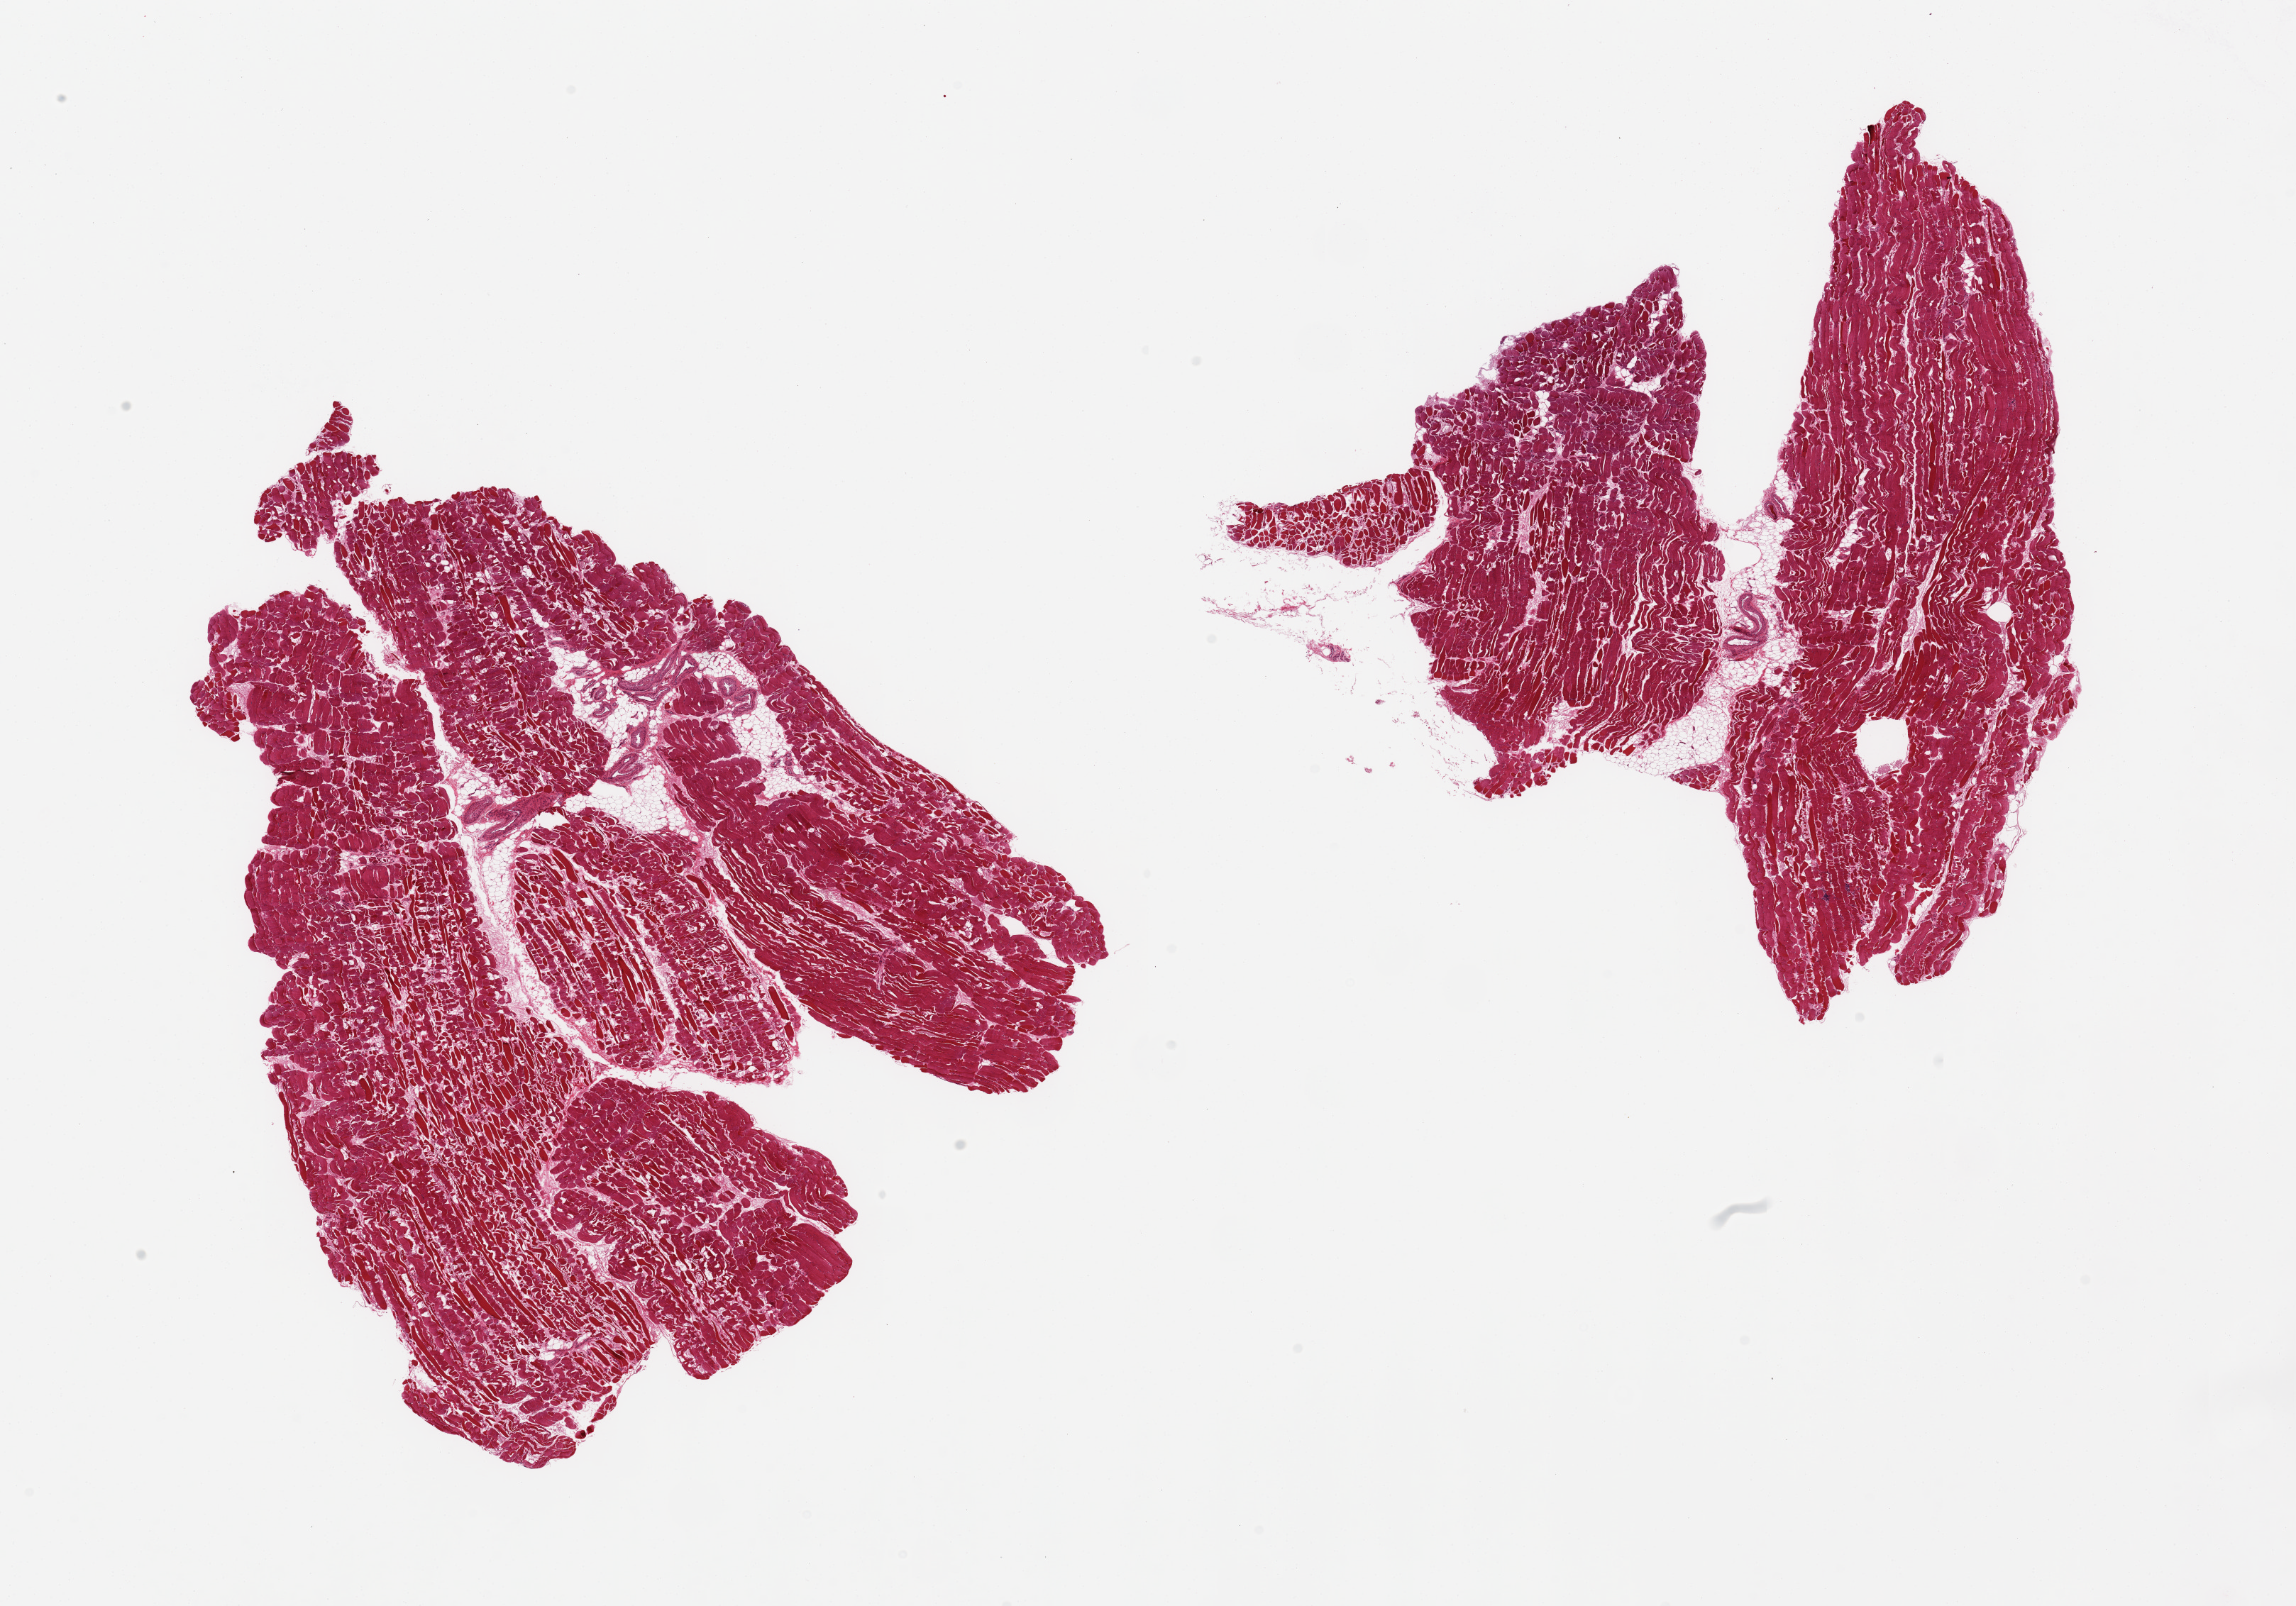
Haematoxylin and eosin whole-slide image, brightfield — low-resolution overview of the scanned area, about 25.6 x 17.9 mm; PAXgene-fixed, paraffin-embedded tissue; sampled site (target tissue): skeletal muscle; tissue donor sample. Donor sex: male.
• pathologist's review note for this sample: 2 pieces; small amount of internal fat and vessels, some atrophy, focal chronic inflammation